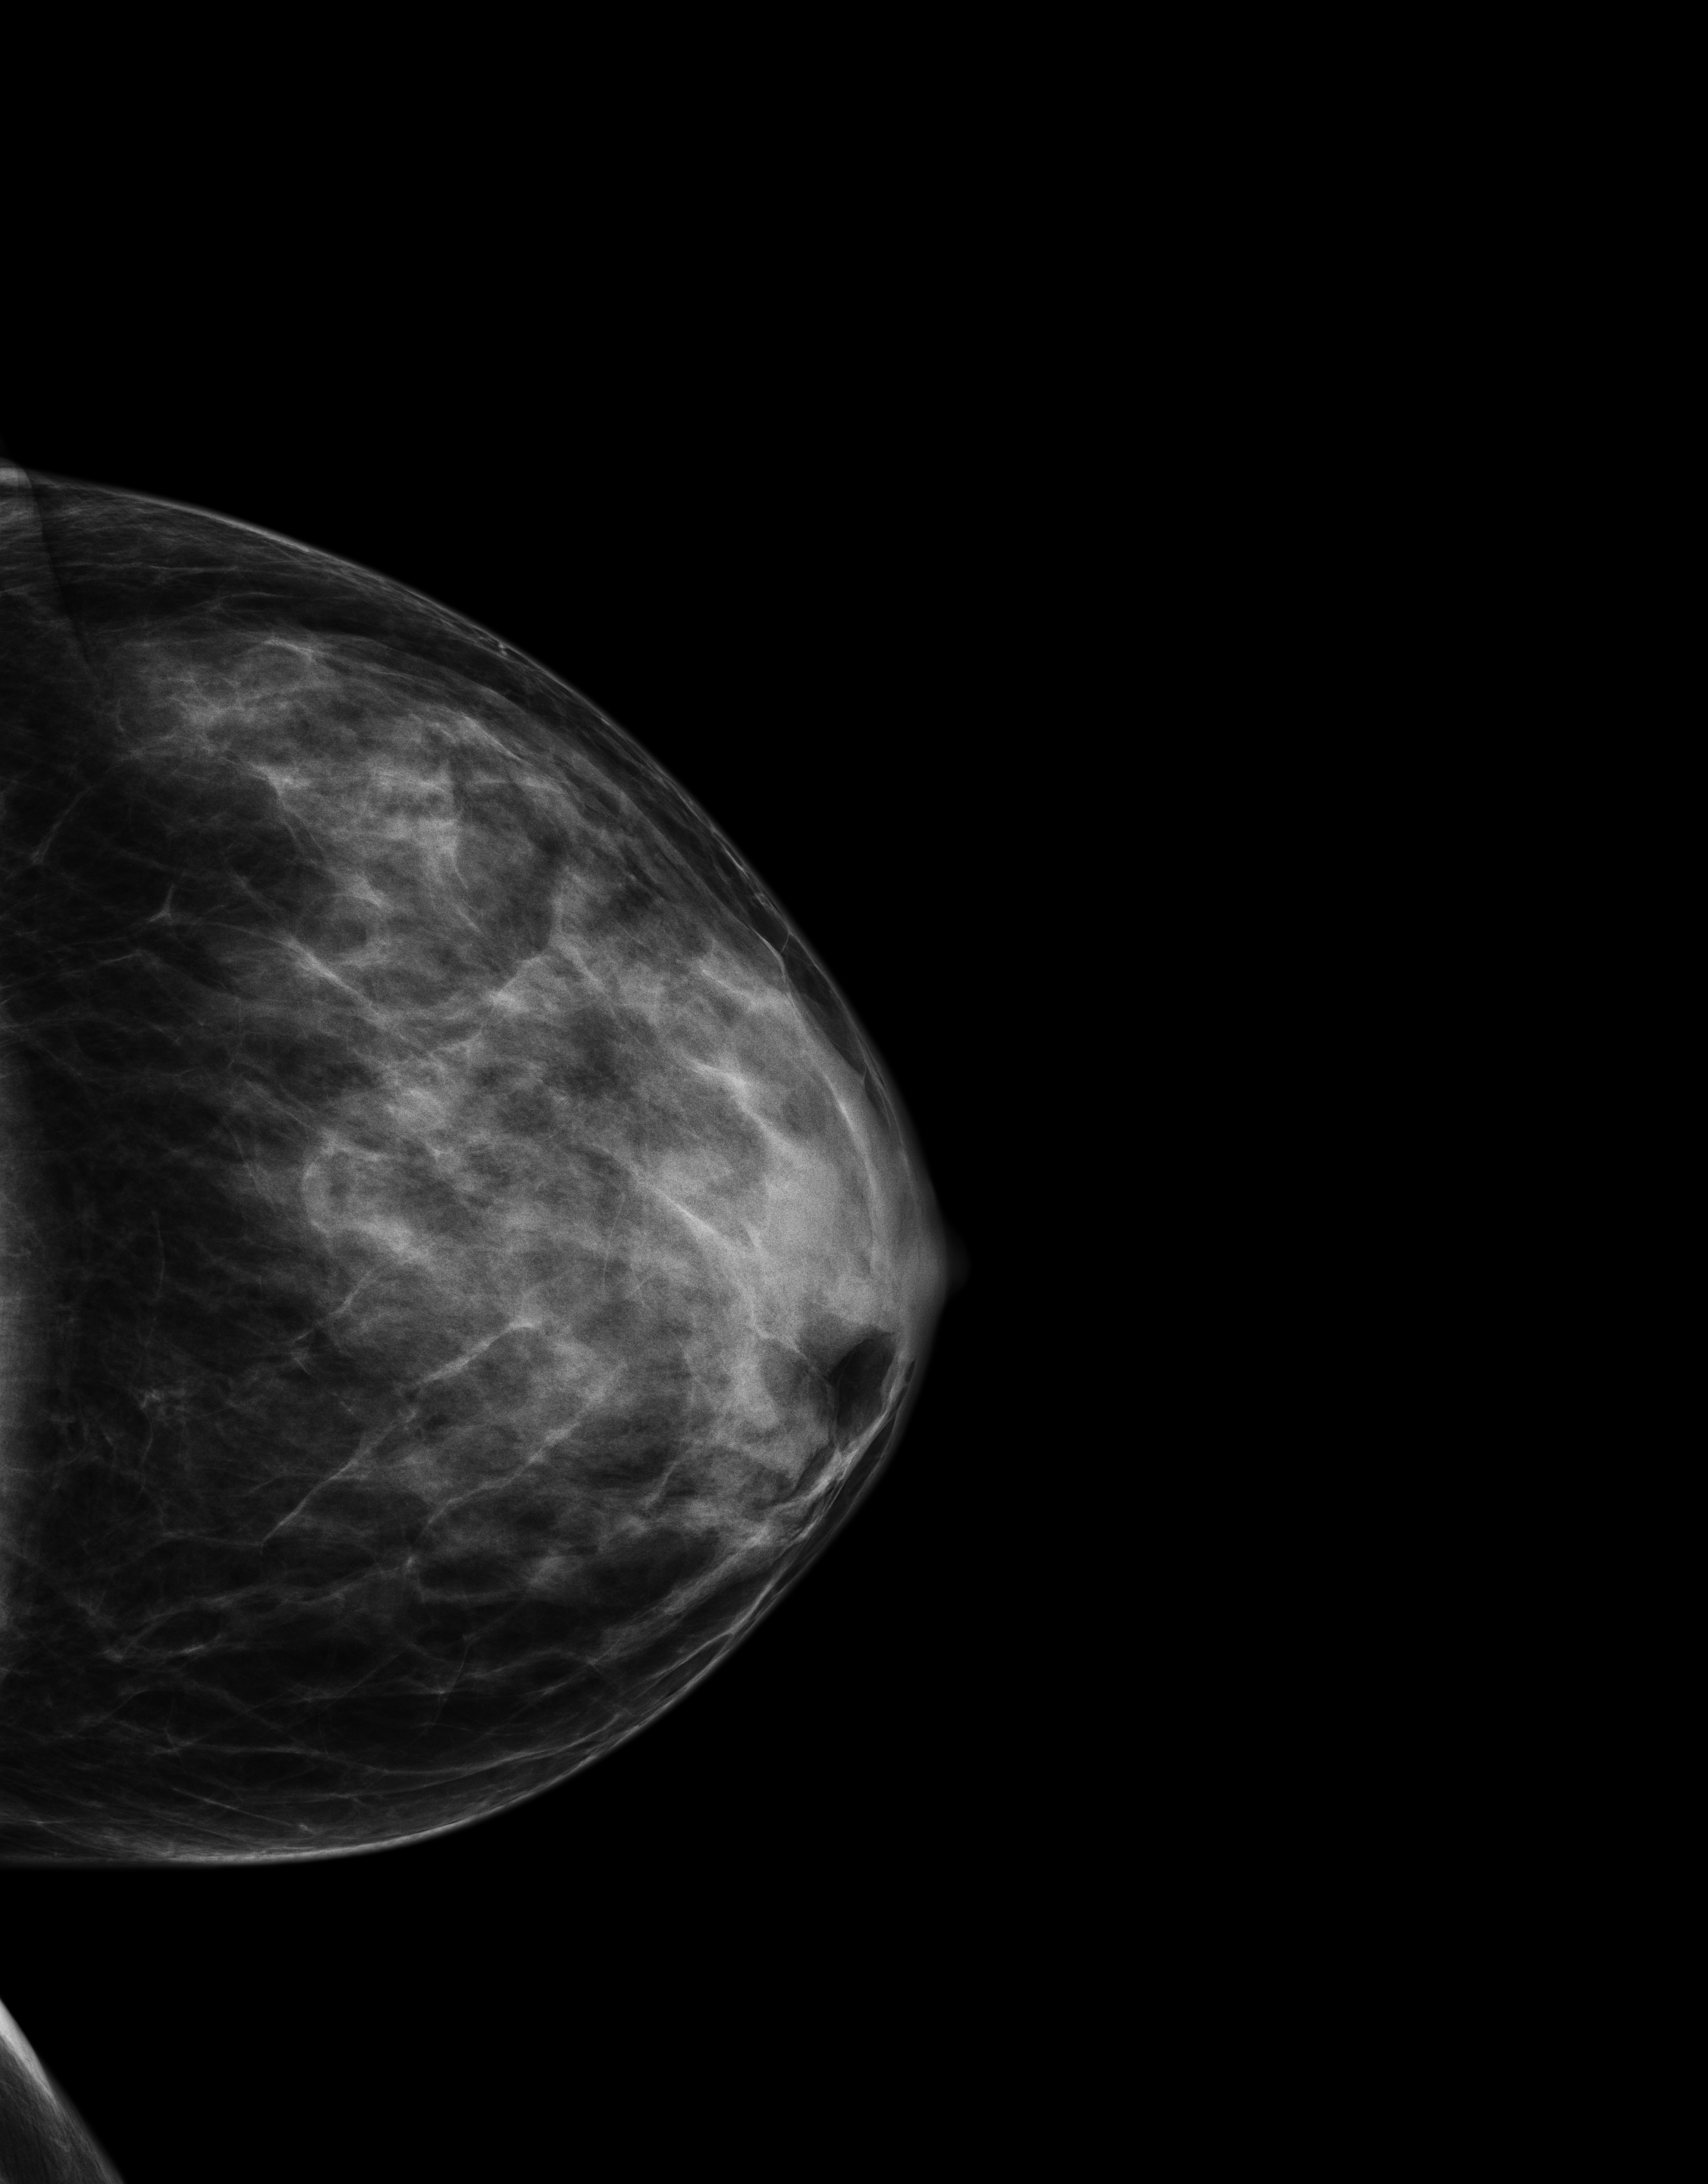
Digital mammogram (FFDM), left breast, cranio-caudal projection, annual screening mammography examination. Patient: female, 48 years.
BI-RADS breast density category at the screening exam (both breasts, scale 1–4): 4. Final BI-RADS category for the screening round (tomosynthesis exam, both breasts): category 2. Recall: recalled for additional imaging after this screen.